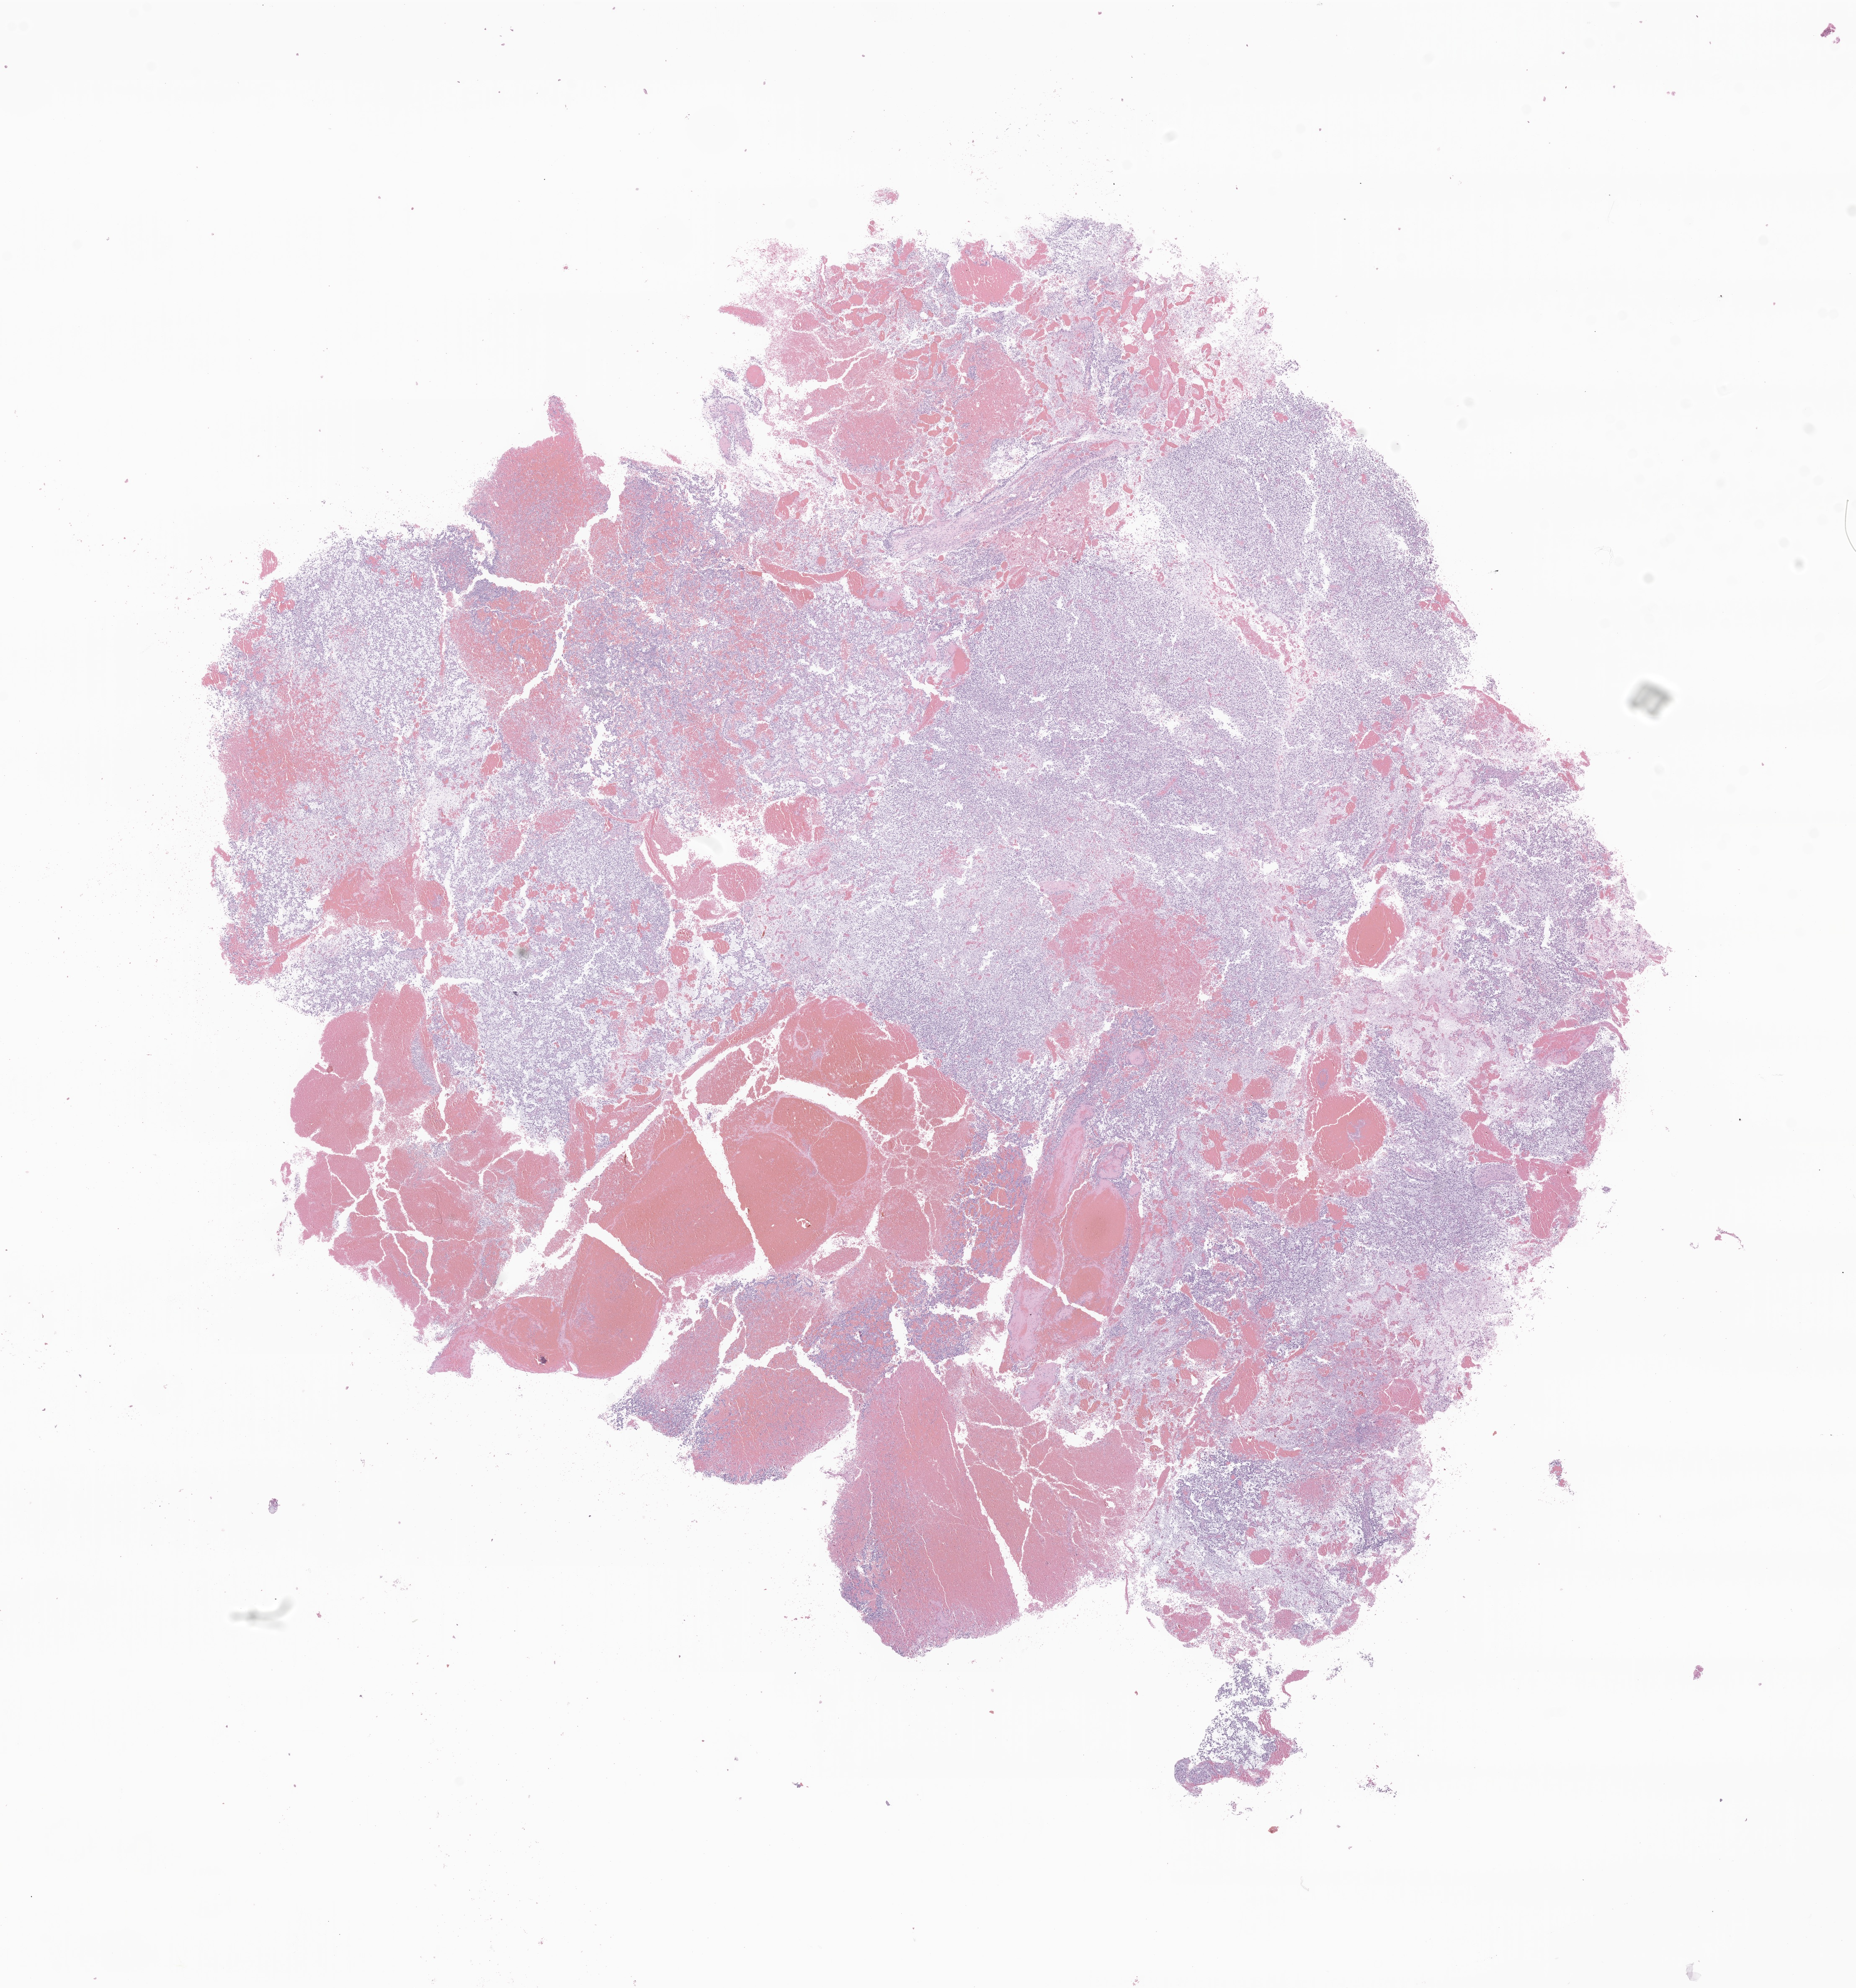
Hematoxylin and eosin (H&E) whole-slide image of tumor tissue from the frontal lobe — a low-resolution overview of the entire scanned area, about 18.7 x 20.0 mm; formalin-fixed, paraffin-embedded (FFPE) tissue. Patient: male, age 67 months (5 years 7 months).
• diagnosis: Glioma, malignant